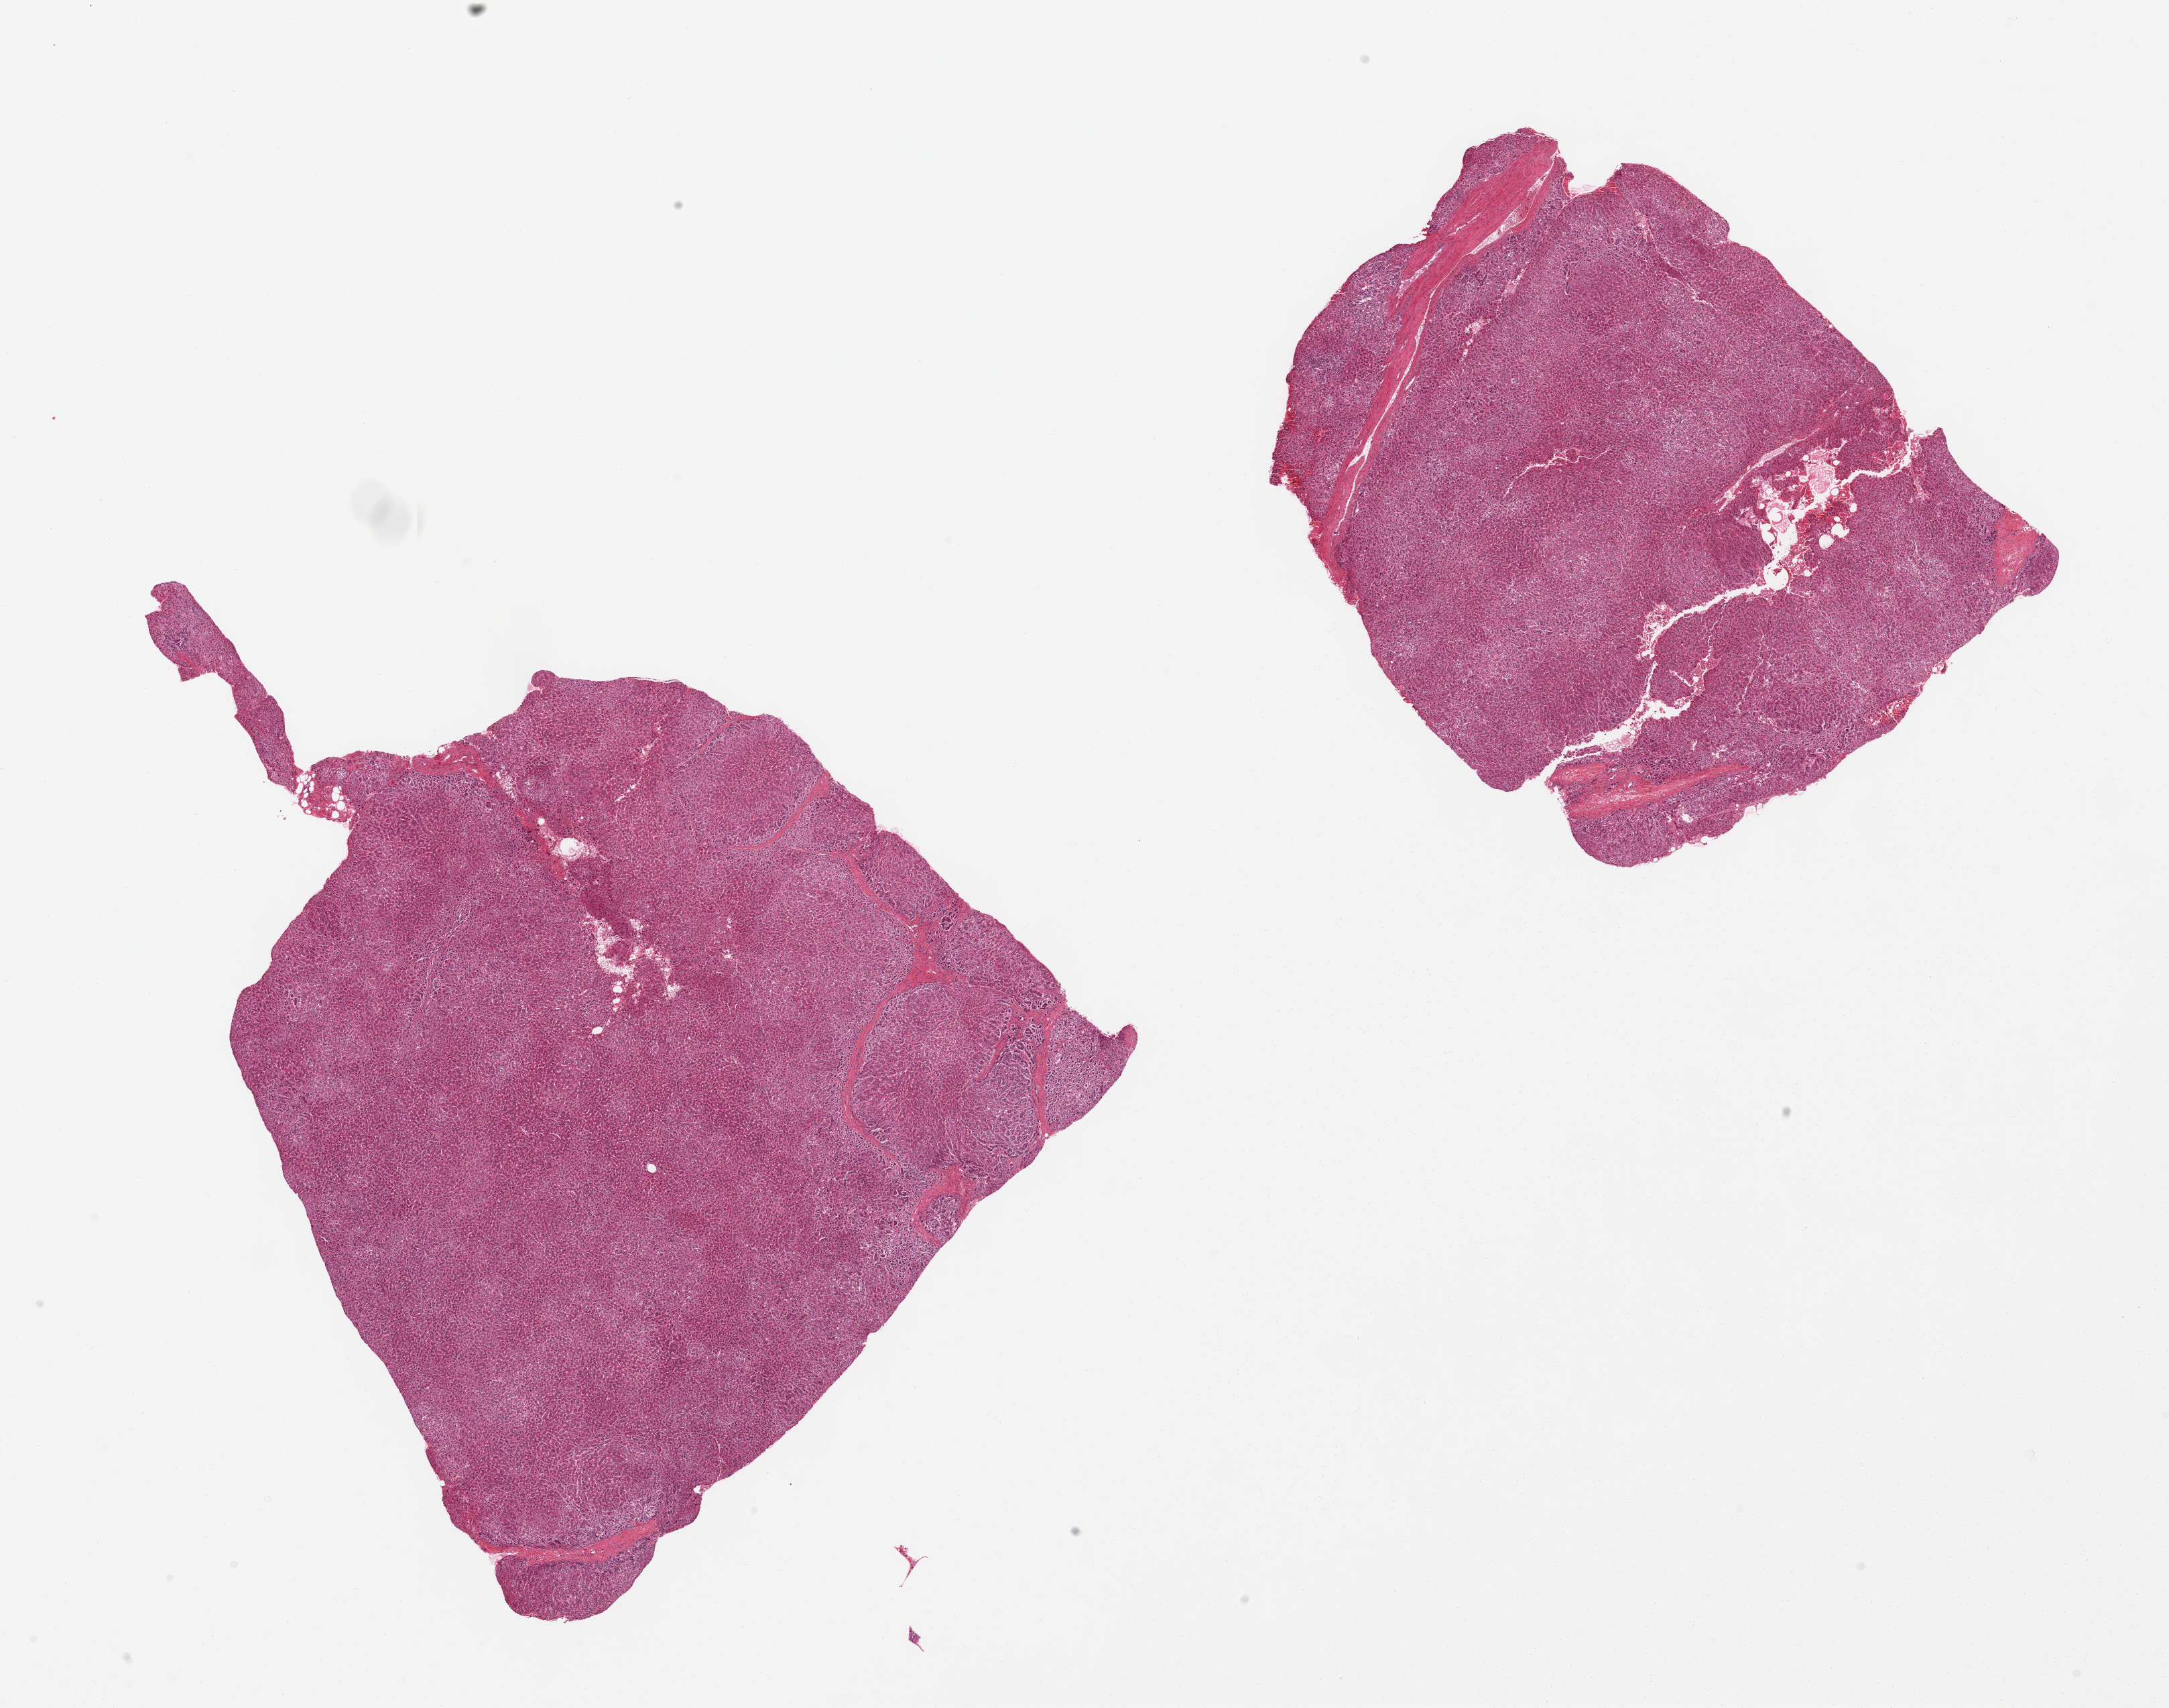
H&E whole-slide image, brightfield — shown as a low-resolution overview of the whole scanned area (about 25.6 x 20.2 mm), PAXgene-fixed, paraffin-embedded tissue, section of adrenal gland (target tissue), donor tissue sample. Donor: female.
* pathologist's review note for this sample: 2 pieces